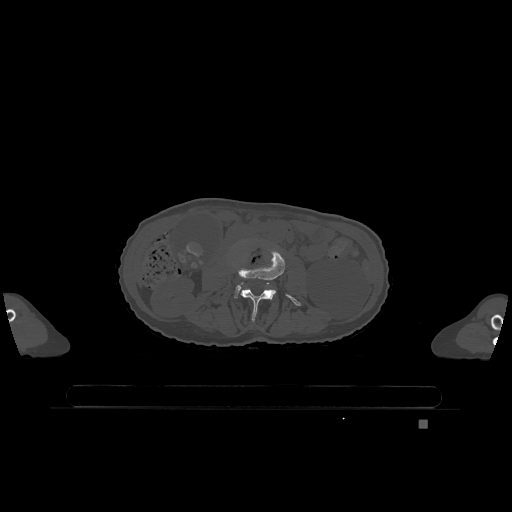
CT including the spine, one axial slice; slice 346 of 1317 in the series (ordered by position); bone window (W 1800 / L 400 HU); 0.5 mm slice thickness; 512 × 512 image matrix, field of view 500 × 500 mm. Patient: female, 74 years. Case-level facts recorded for this patient, not image findings: primary cancer: lung; vertebrae with lytic lesions (as recorded): T1, T4, T5, T6, L4, L5.
Outlined on this slice (semi-automatically segmented with operator editing):
- L3 vertebra: box from (x=238, y=249) to (x=301, y=321) px
- L4 vertebra: (x=234, y=285)–(x=272, y=300)